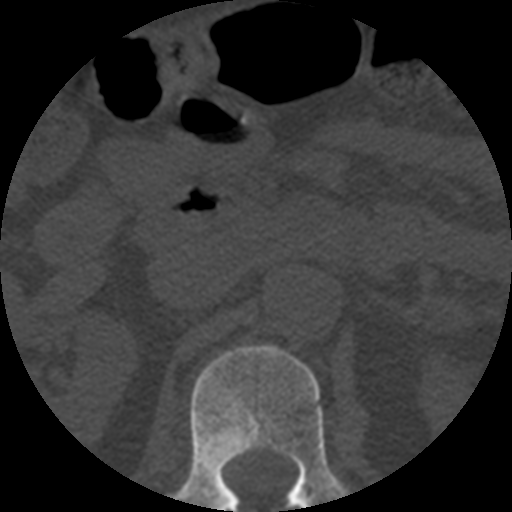
CT including the spine, one axial slice. Slice 186 of 508 in the series (ordered by position). Reconstruction kernel STANDARD. 120 kVp. Bone window (W 1800 / L 400 HU). 512 × 512 image matrix. Patient age 57 years. From the clinical record (not read from this slice): primary cancer: prostate.
Outlined on this slice (semi-automatic segmentation, software-assisted and operator-edited):
- L1 vertebra: bounding box (x1, y1, x2, y2) in pixels: (173, 345, 349, 512)